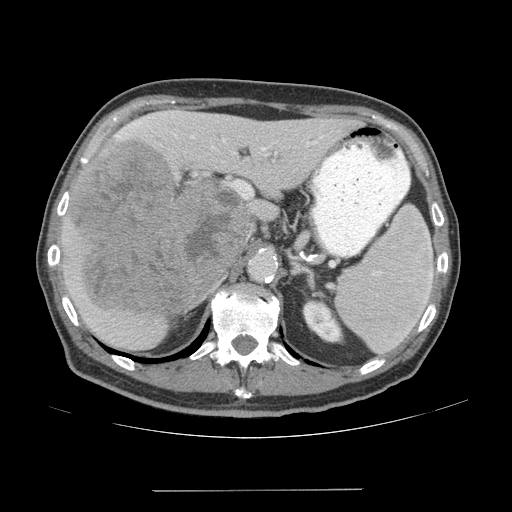
Contrast-enhanced abdominal CT (liver protocol), one axial slice. Position 38 of 77 along the scan axis. Reconstruction kernel STANDARD. Soft-tissue window (W 400 / L 40 HU). 2.5 mm slice thickness. 512 × 512 image matrix. Case-level facts recorded for this patient, not image findings: diagnosis: hepatocellular carcinoma (patient treated with transarterial chemoembolisation; whether this scan precedes or follows treatment is not stated here); TNM stage (as recorded): Stage-IVA; Child-Pugh class: A; tumour nodularity: uninodular.
Annotated regions visible in this slice (semi-automatically segmented with operator editing):
- liver parenchyma outside the tumour (the mass and vessels are separate outlines, so this box may not span the whole liver): bounding box (x1, y1, x2, y2) in pixels: (60, 108, 360, 350)
- mass: (70, 143, 251, 316)
- liver vessels: (115, 114, 323, 151)